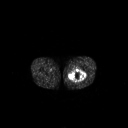
FDG PET of an extremity soft-tissue mass (from a PET/CT study), one axial slice. Position 246 of 267 along the scan axis. 3.27 mm slice thickness. 128 × 128 image matrix, field of view 700 × 700 mm. Male patient, age 44 years. Case-level facts recorded for this patient, not image findings: histological type: undifferentiated pleomorphic liposarcoma; grade: high; site of the primary tumour: left thigh.
Outlined on this slice (expert contour drawn on MRI and transferred to this co-registered scan by the dataset authors):
- gross tumour volume including surrounding oedema: bounding box [x1, y1, x2, y2] px = [67, 69, 86, 83]
- gross tumour volume (mass): [69, 69, 86, 81]